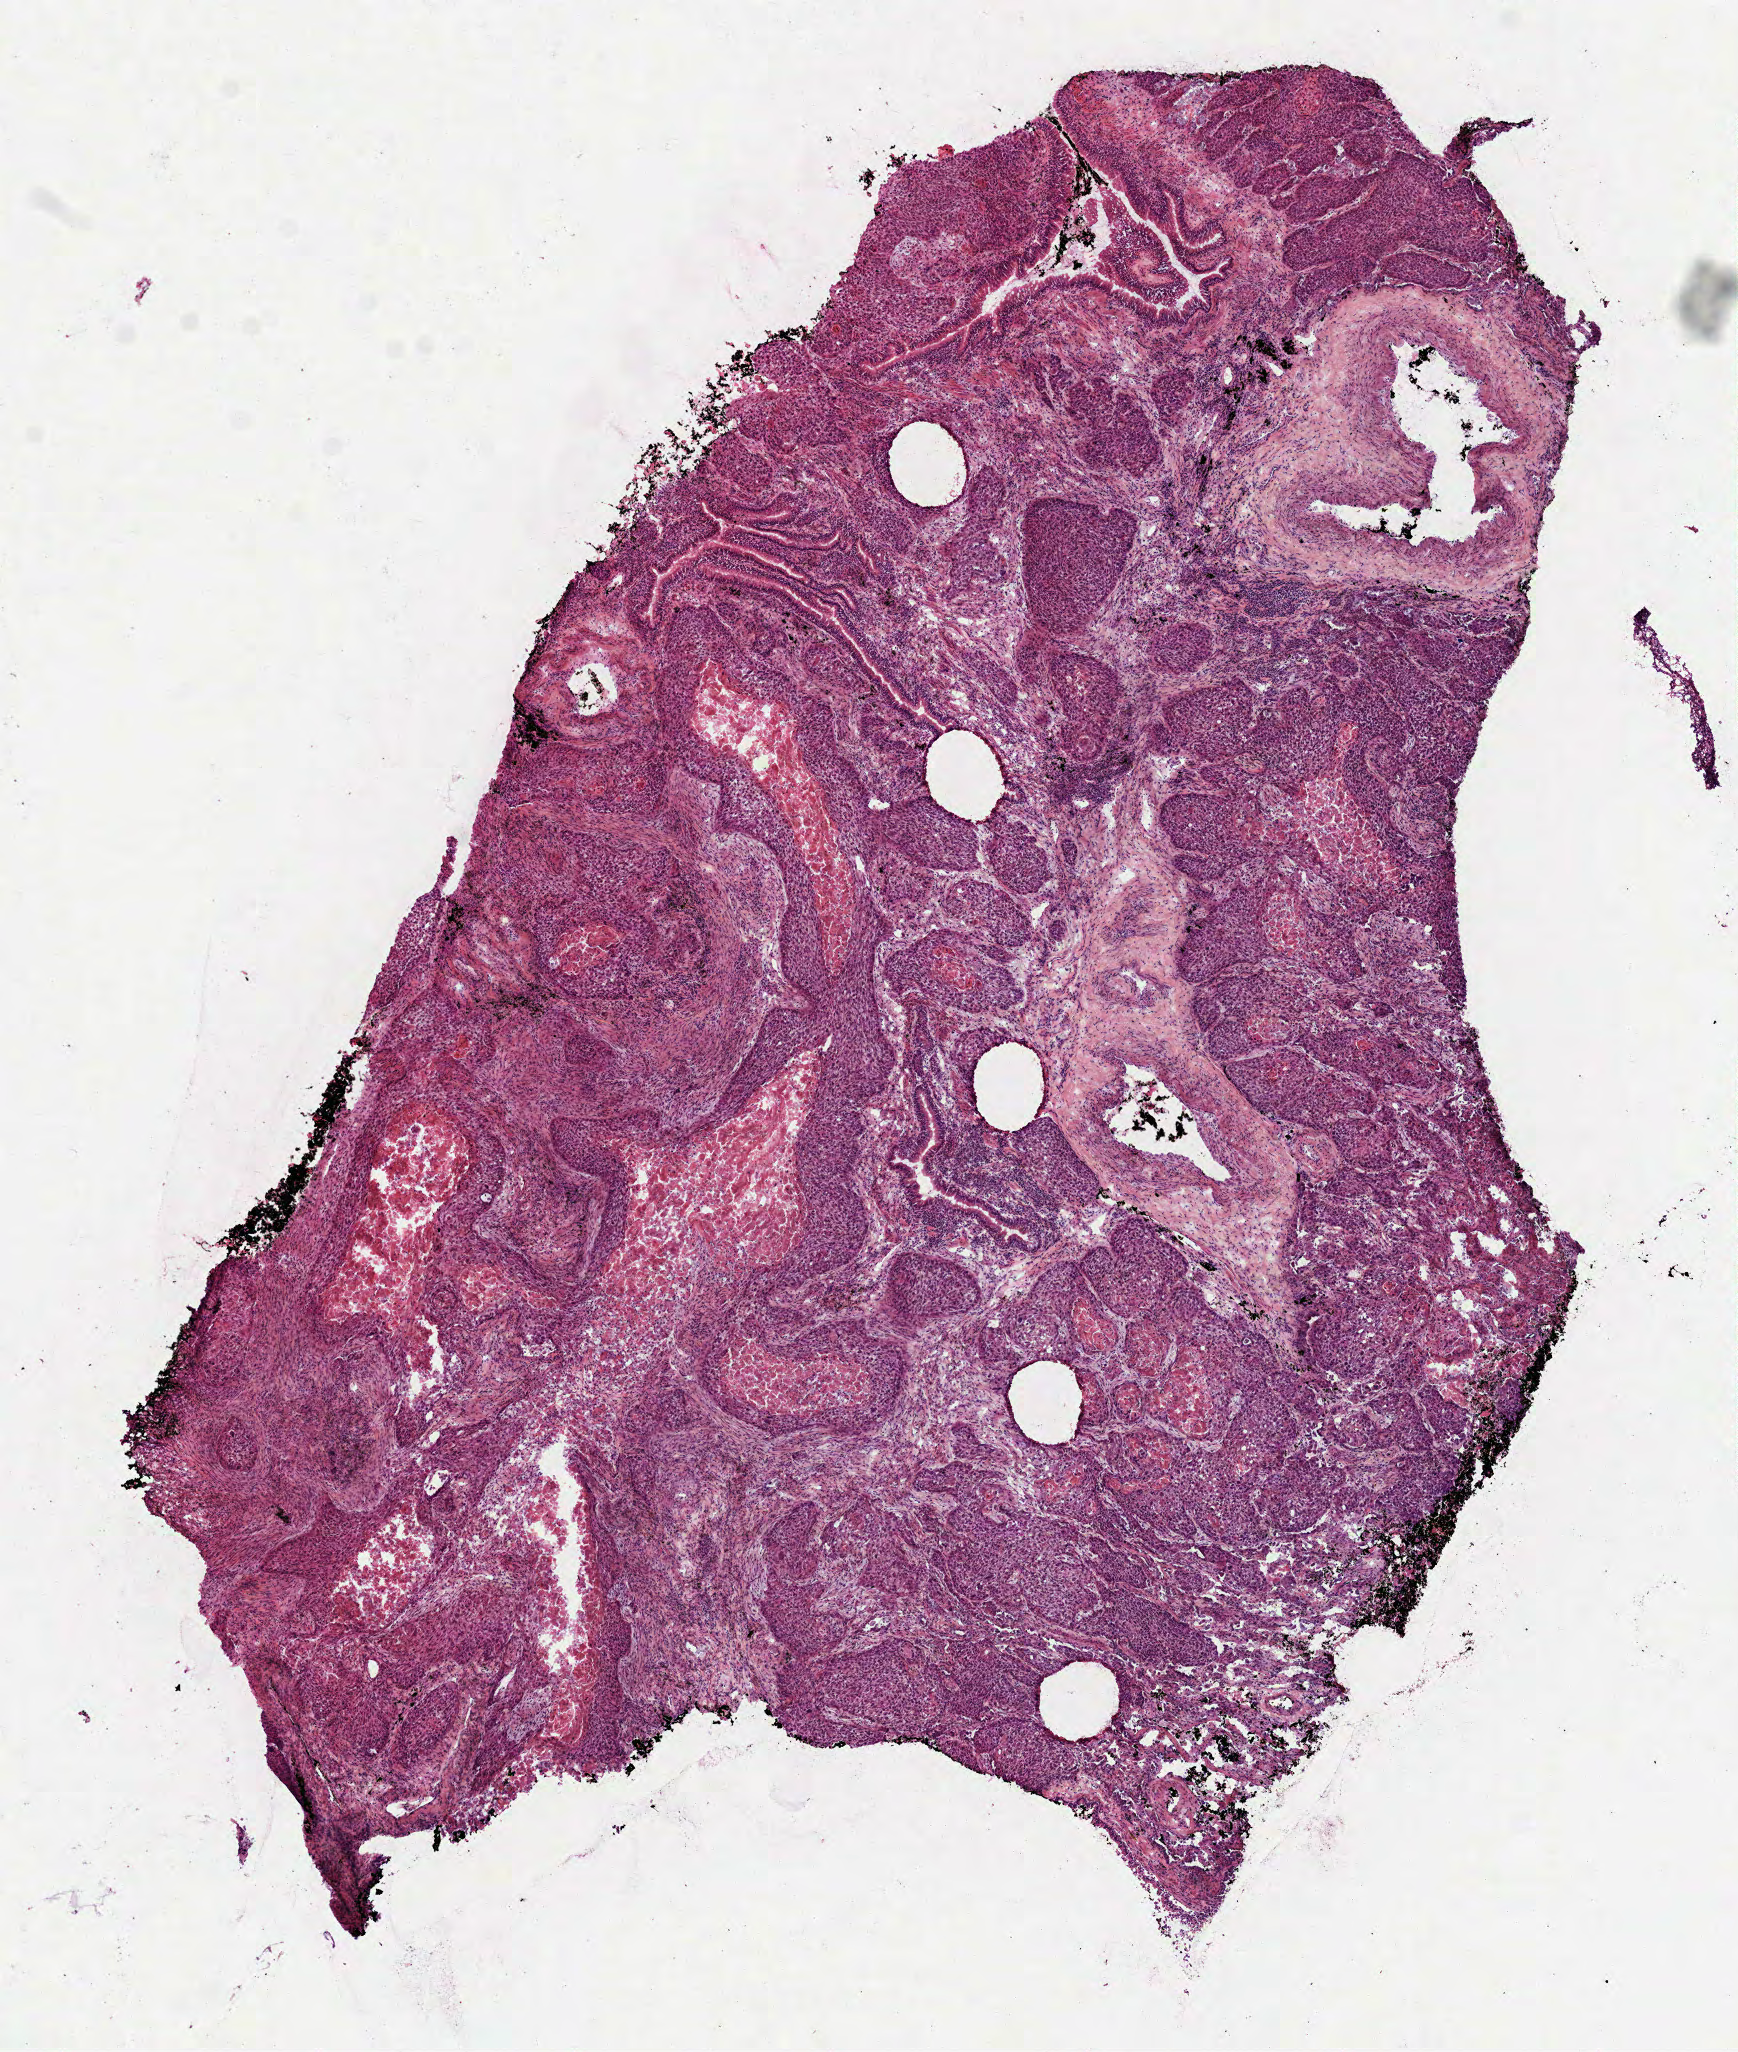
Digitized Hematoxylin and eosin (H&E) stained tissue section (whole slide), a low-resolution overview of the entire scanned area, about 7.0 x 8.3 mm (from a 40x scan), frozen section from the top of the tissue portion, primary tumour sample from the lung. Patient: male, age at initial diagnosis 79 years. Composition of this section per pathologist review: tumour cells 82%, tumour nuclei 75%, normal cells 0%, stromal cells 15%, necrosis 3%.
Diagnosis: Squamous cell carcinoma, NOS (lower lobe, lung). AJCC pathologic stage: IB (7th edition). TNM: T2 N0 M0.